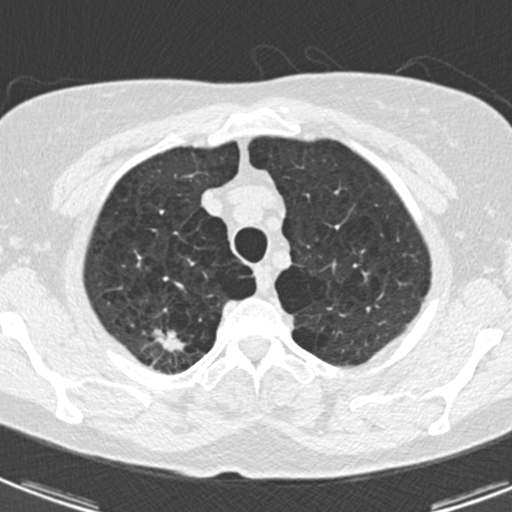
Low-dose screening chest CT, one axial slice; slice 150 of 174 in the series (ordered by position); 120 kVp; lung window (W 1500 / L -600 HU); 2 mm slice thickness; 512 × 512 image matrix, field of view 281 × 281 mm.
Structures marked on this image (manually delineated by an expert):
- lesion 1 (tumor, upper lobe of right lung): bounding box (x1, y1, x2, y2) in pixels: (154, 329, 186, 352)